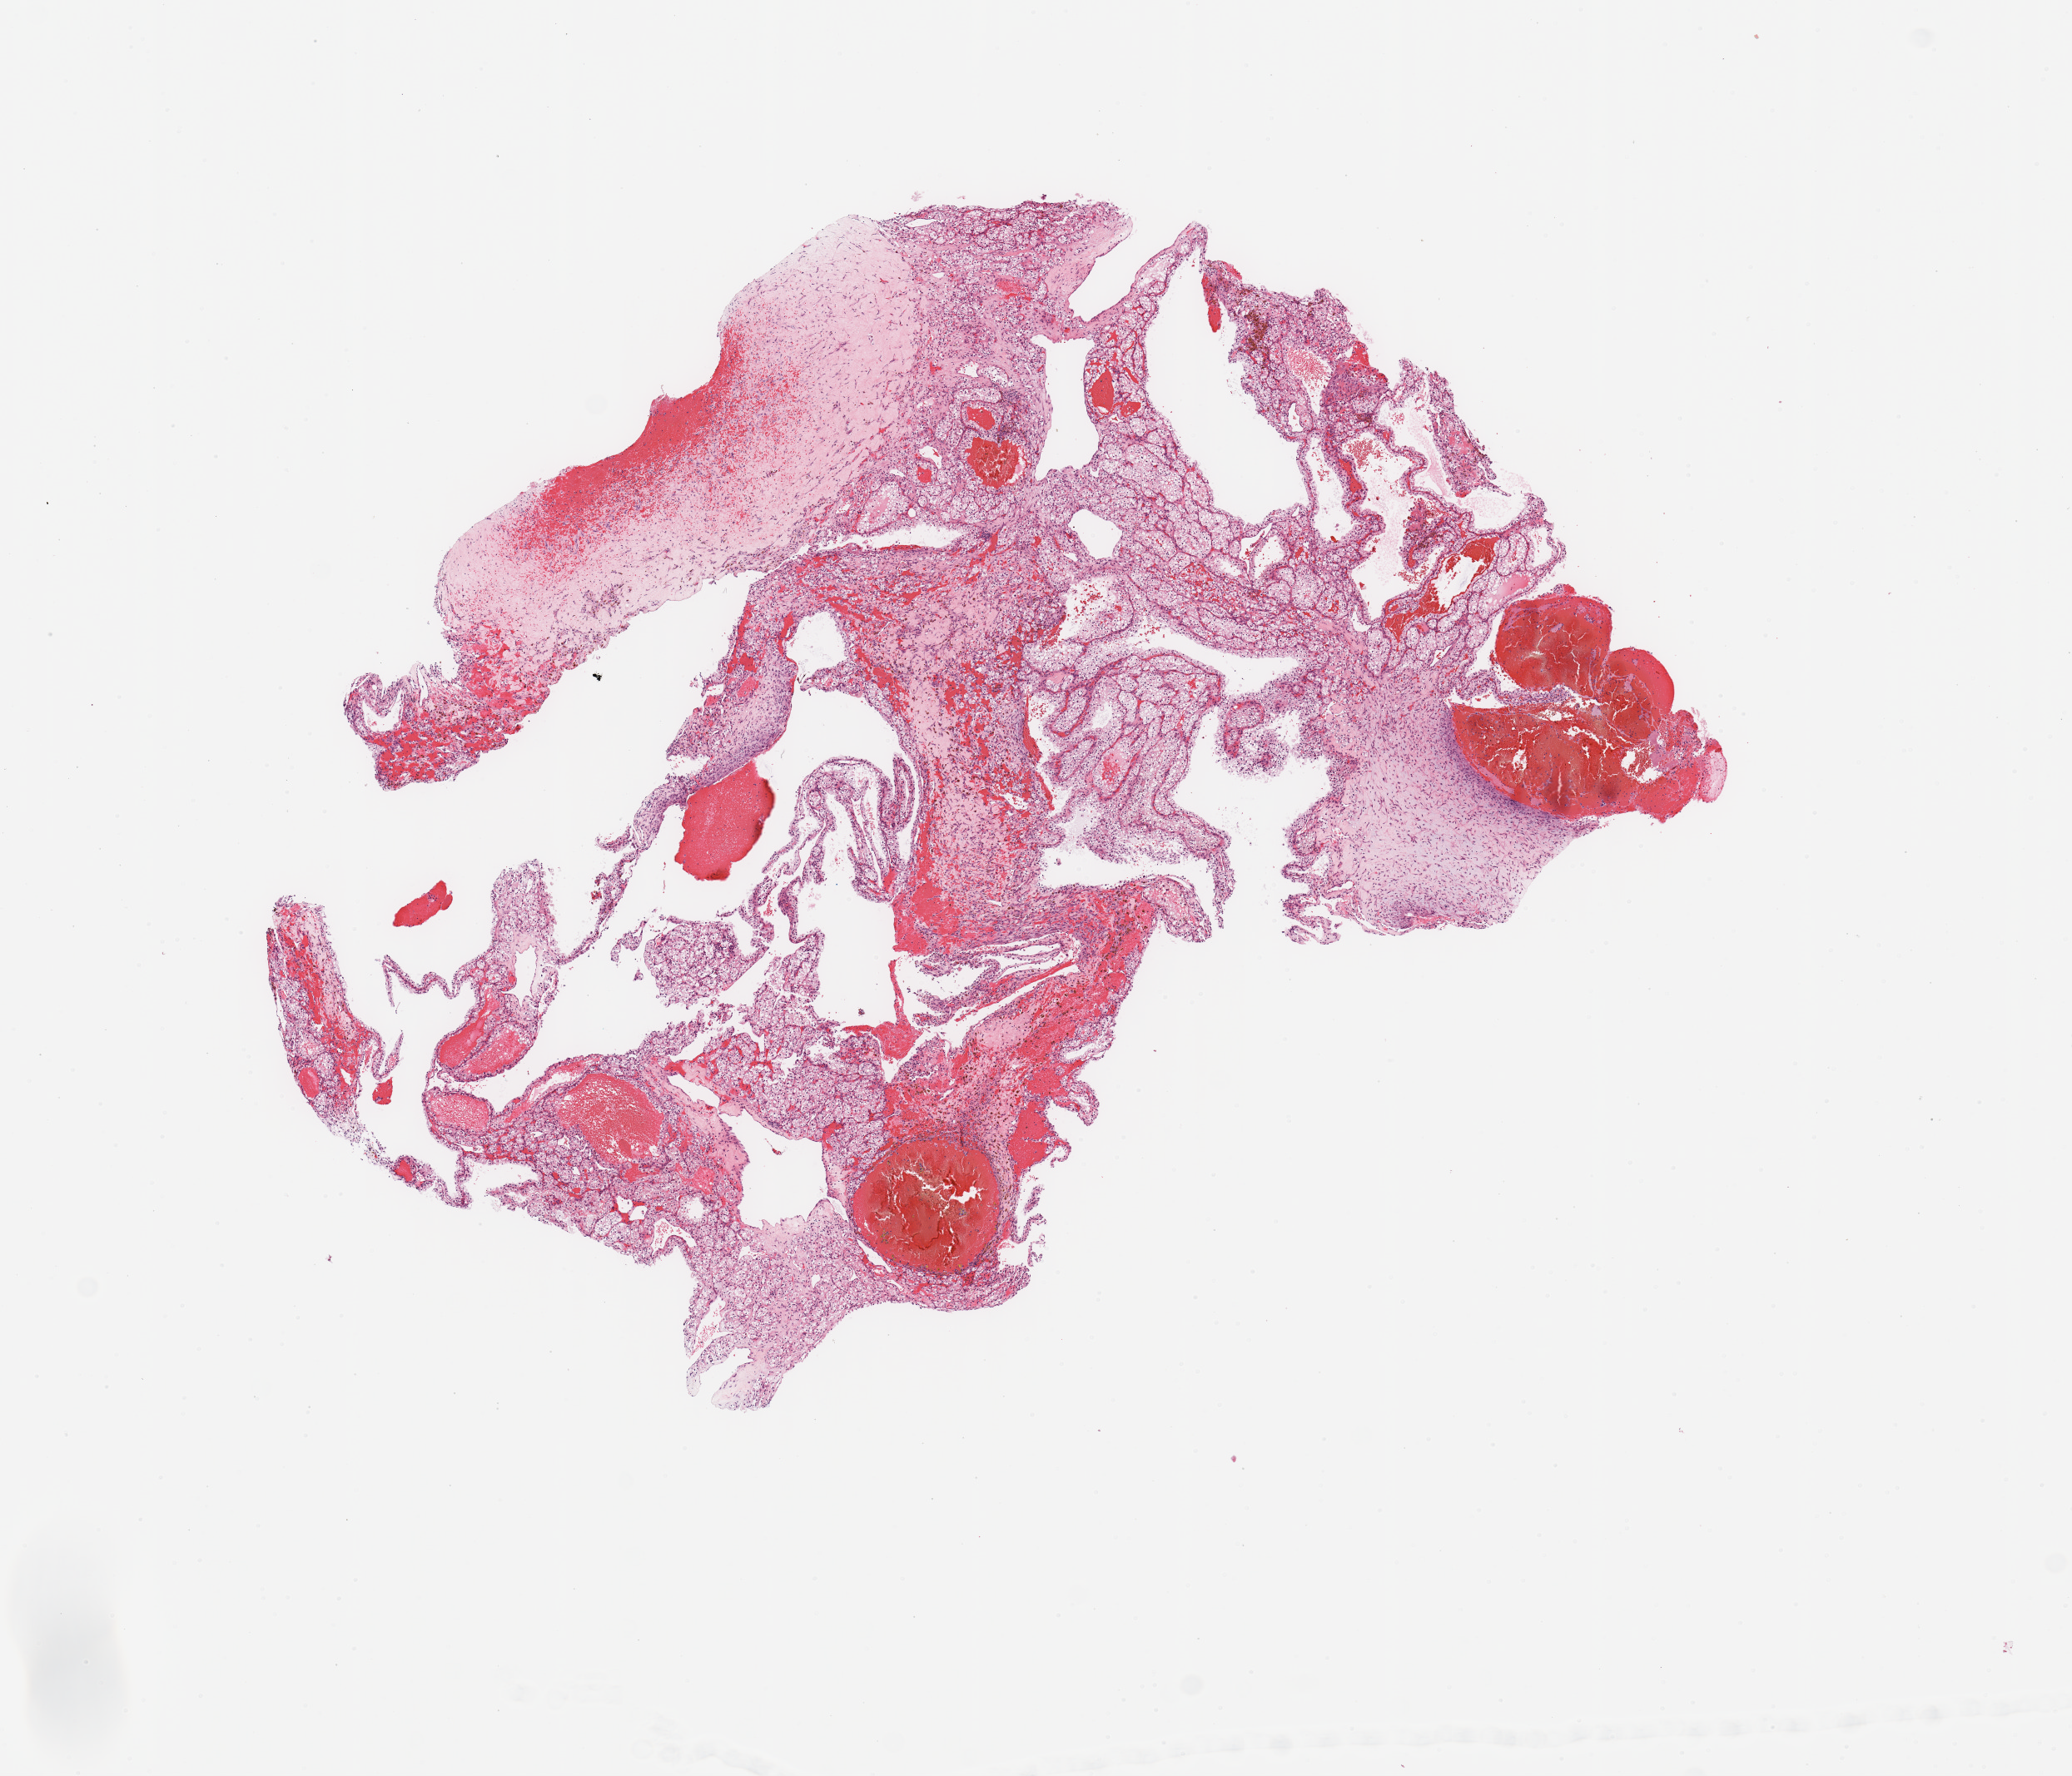
Hematoxylin and eosin (H&E) stained whole-slide image, a low-resolution overview of the entire scanned area, about 9.8 x 8.4 mm (from a 20x scan), tumour tissue sample, sampled site: kidney. 57-year-old male patient. Histologic grade: G3 (poorly differentiated). Slide review estimates, as recorded: tumour nuclei 80%, necrosis 10%.
AJCC pathologic stage: I. Diagnosis: Renal cell carcinoma, NOS. Primary tumour site (as recorded): upper pole.